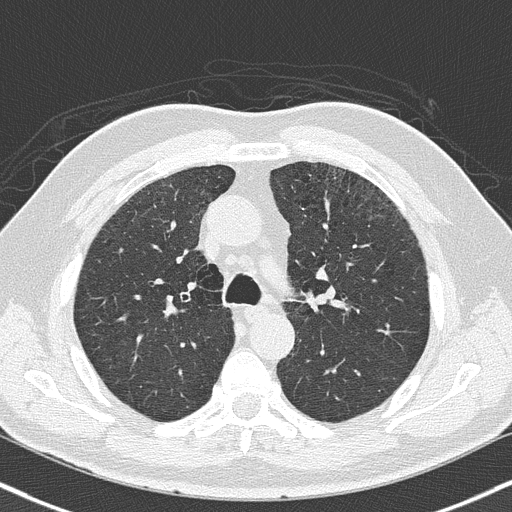
Axial slice from a low-dose chest CT screening exam, second screening round (one year after baseline), lung window (W 1500 / L -600 HU), 2 mm slice thickness, 120 kVp. Male participant, aged 64 years at enrolment.
• Expert-annotated lung lesion, box from (x=312, y=282) to (x=345, y=311) px.
• Screening reader's record for this exam: no non-calcified nodule ≥4 mm recorded.
• Participant outcome: lung cancer diagnosed 72 days after this screen — squamous cell carcinoma, keratinizing, NOS, left upper lobe, moderately differentiated (G2), stage IA (AJCC 6th edition), 4 mm at pathology.